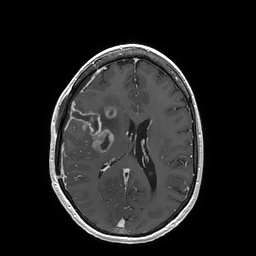
Brain MRI from a brain-tumour surgery series, one axial slice; slice 73 of 202 in the series (ordered by position); T1-weighted post-contrast; 1 mm slice thickness; 256 × 256 image matrix, field of view 250 × 250 mm. Case-level facts recorded for this patient, not image findings: histopathology: Glioblastoma; WHO grade: 4; IDH mutation: no; tumour location: Right Insular.
Outlined on this slice (manually delineated by an expert):
- tumour: bounding box [x1, y1, x2, y2] px = [69, 108, 115, 152]